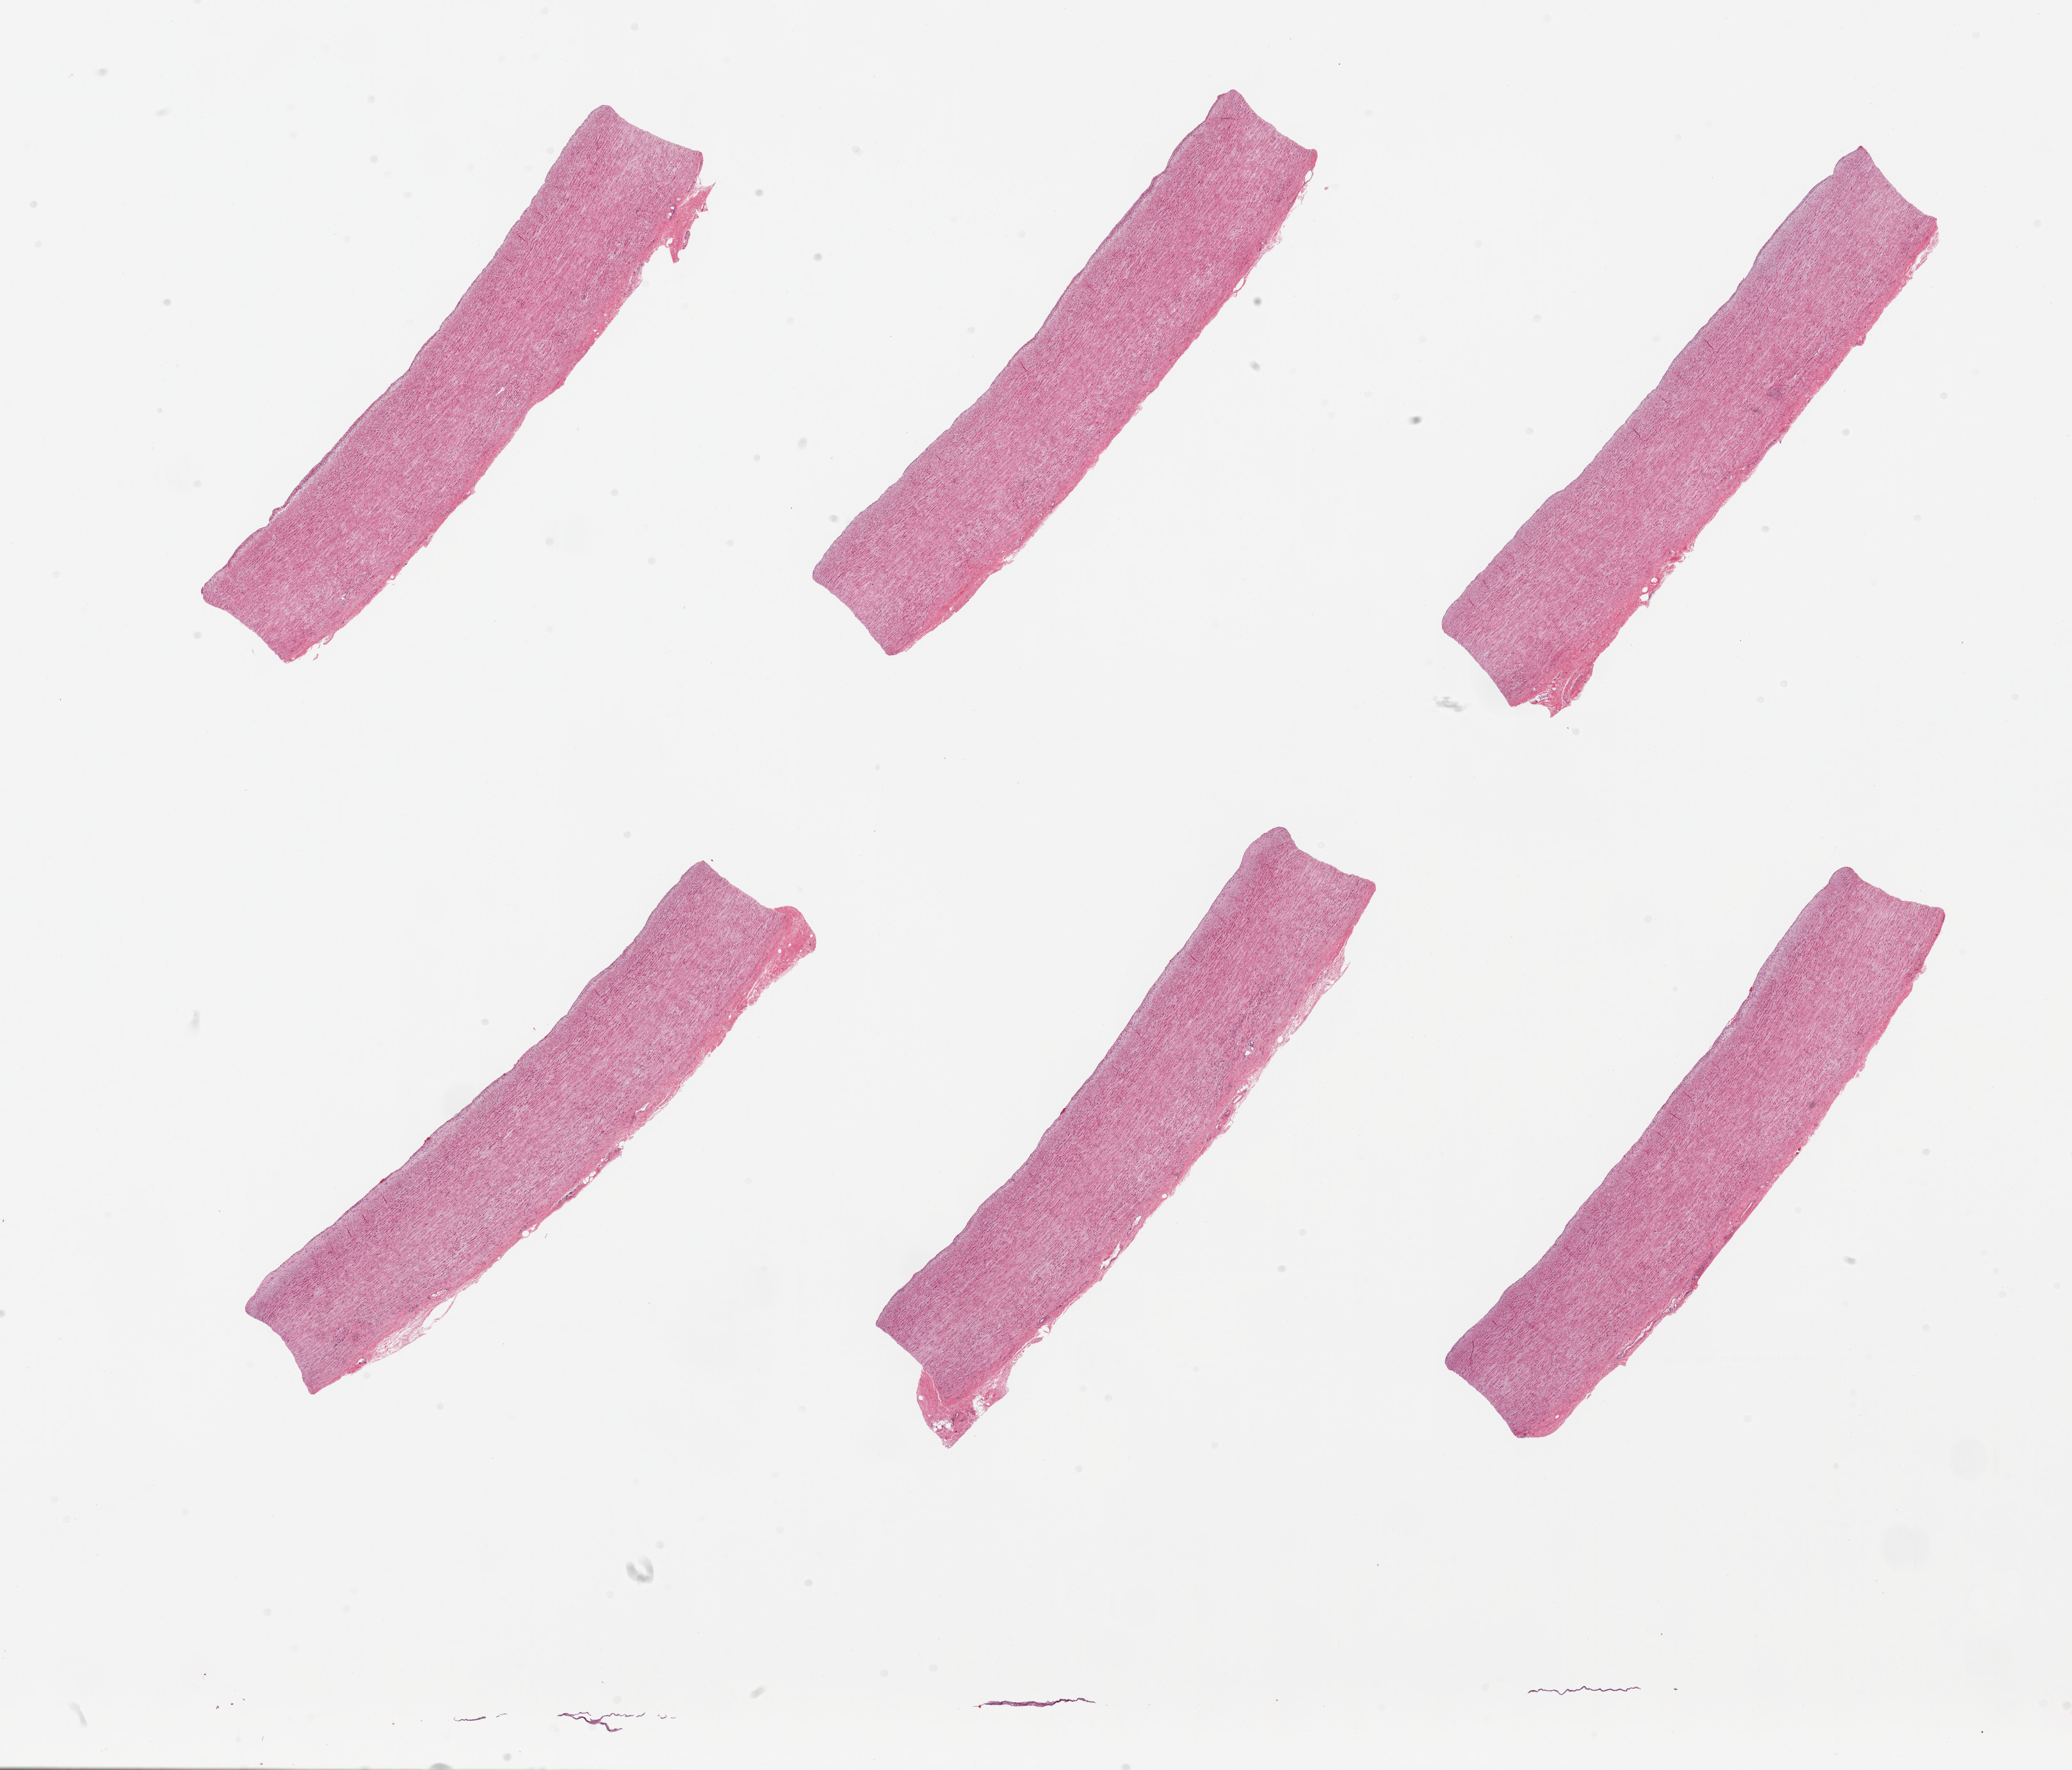
Whole-slide image, hematoxylin and eosin (H&E) stain, shown as a low-resolution overview of the whole scanned area (about 25.6 x 21.9 mm, from a 20x scan), PAXgene-fixed, paraffin-embedded tissue, sampled site (target tissue): aorta, donor tissue sample.
- reviewer comment on this tissue sample: 6 pieces, minimal atherosis